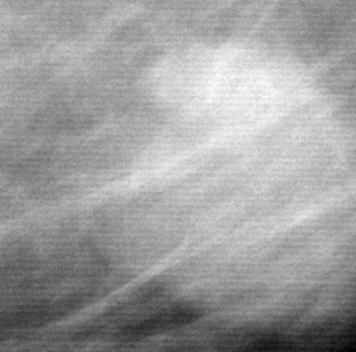
Cropped region of a digitized screen-film mammogram centred on a radiologist-marked abnormality, right breast, MLO view.
Finding: mass, shape oval, margins microlobulated; BI-RADS assessment category 4; subtlety rating 5 on a 1 (subtle) to 5 (obvious) scale; pathology (as recorded): malignant.